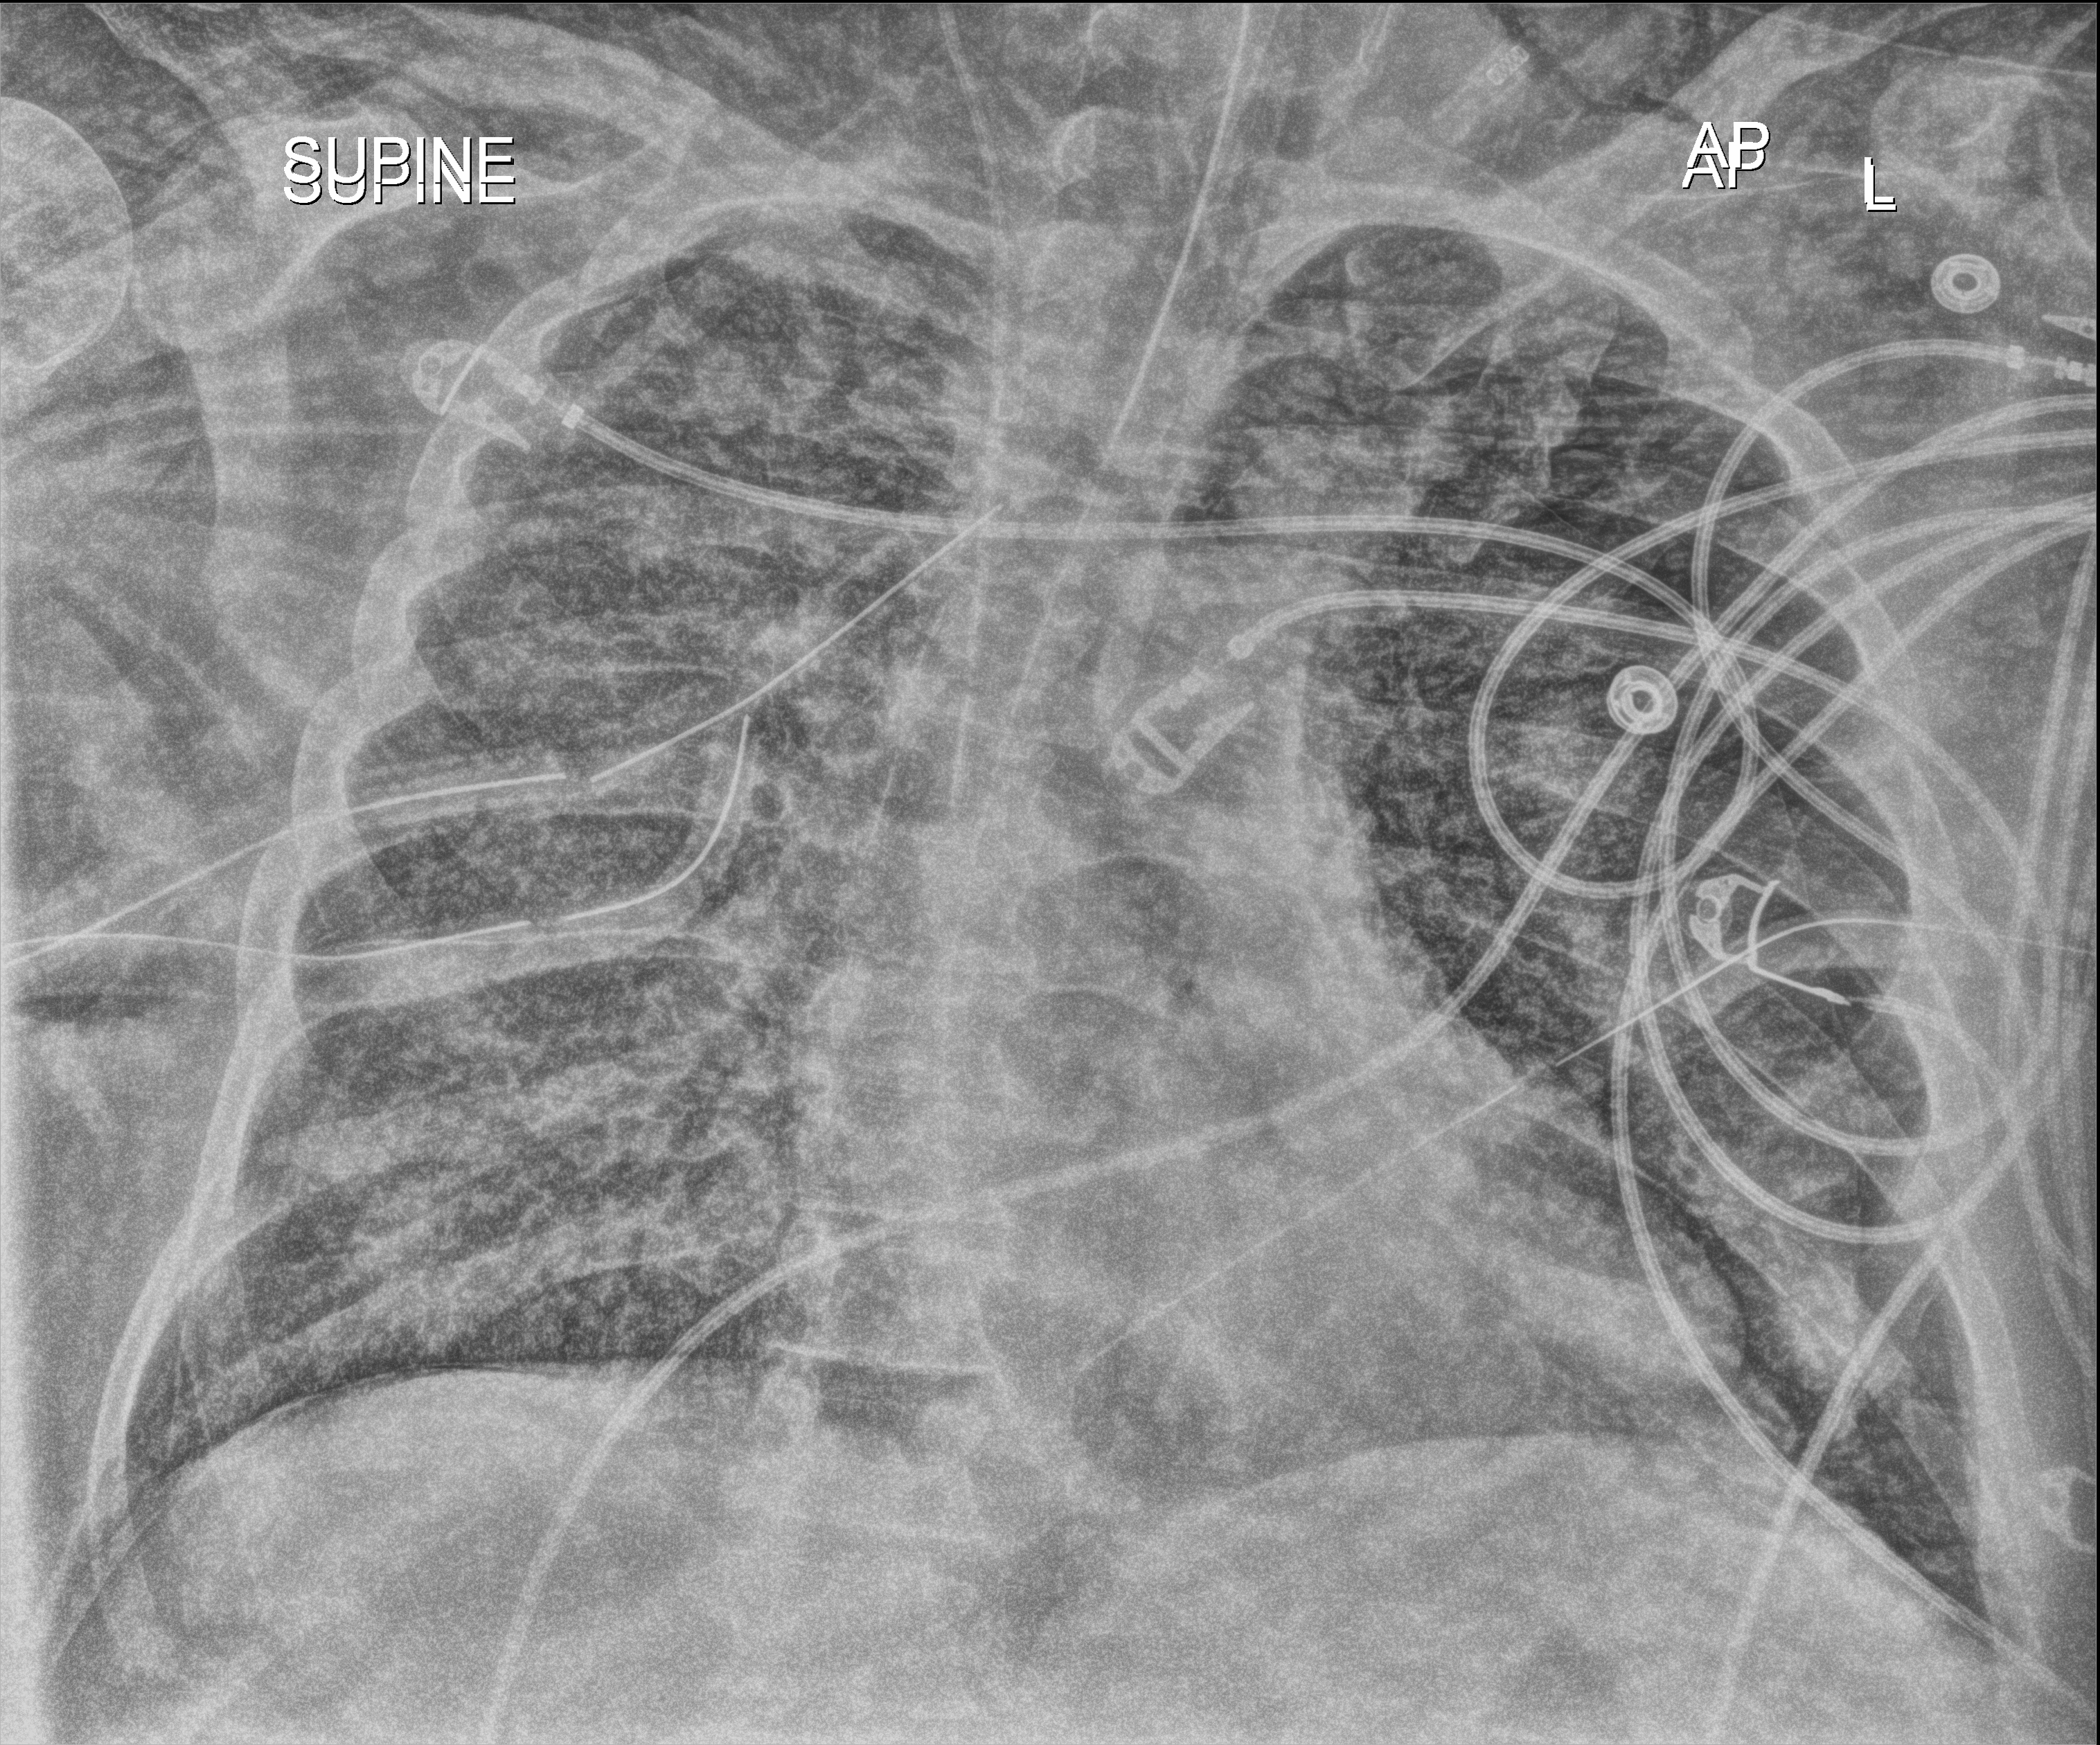
Portable chest radiograph; anteroposterior (AP) projection. Patient hospitalised with COVID-19, aged 18–59 years.
From the hospital-stay record, not from the radiograph (when in the stay this image was taken is not recorded):
- mechanically ventilated during this hospital stay: yes
- admitted to intensive care during this hospital stay: yes
- length of hospital stay: 26 days